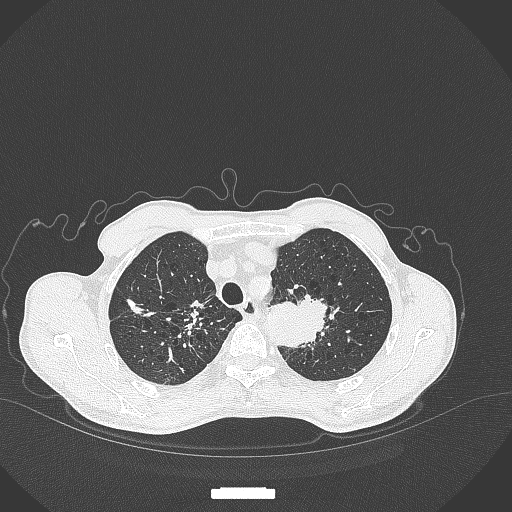
Chest CT, one axial slice. Position 347 of 386 along the scan axis. Lung window (W 1500 / L -600 HU). 512 × 512 image matrix, field of view 400 × 400 mm. Male patient, age 65 years. From the clinical record (not read from this slice): clinical TNM (as recorded): T2b N0 M0.
Structures marked on this image (bounding box drawn by a radiologist):
- lung tumour (recorded histology: adenocarcinoma): bounding box [x1, y1, x2, y2] px = [262, 285, 329, 350]